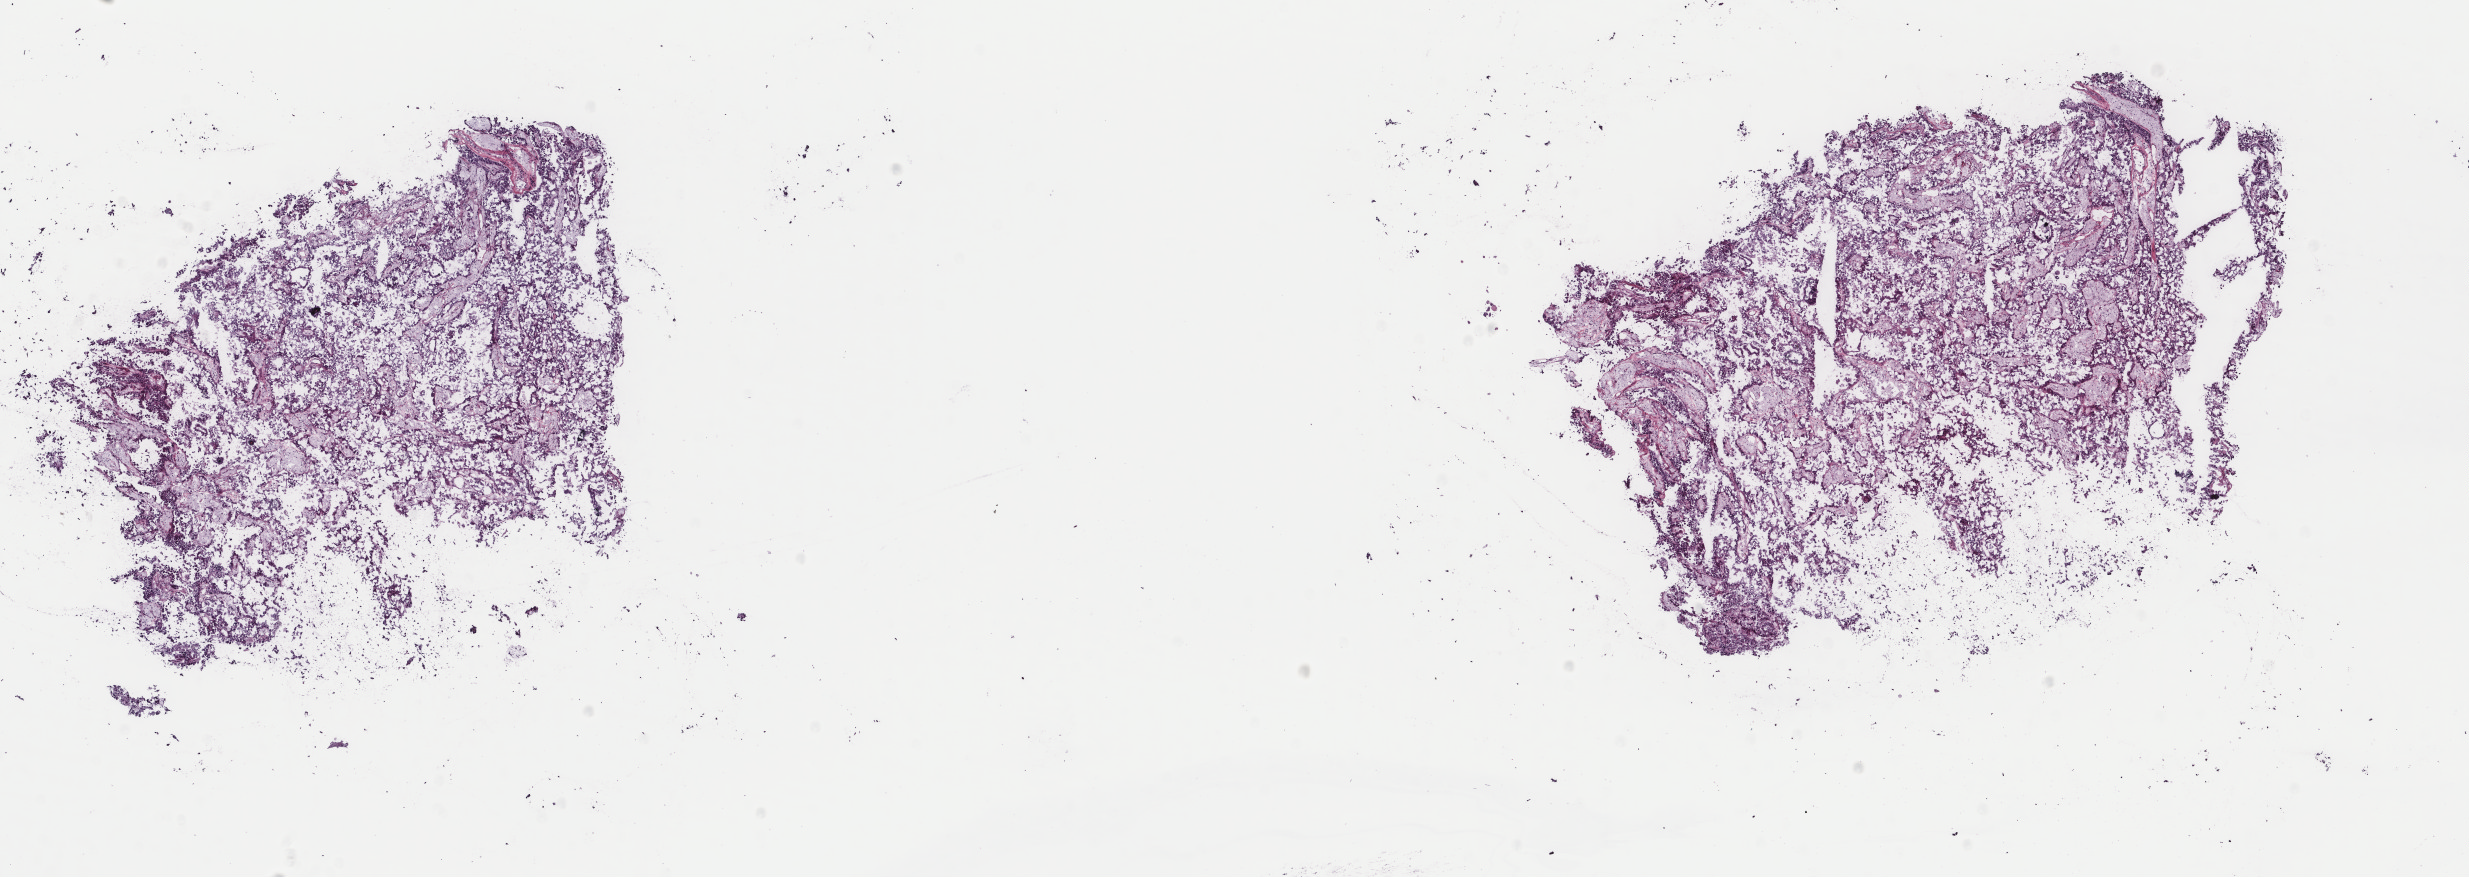
Digitized H&E-stained tissue section (whole slide) — low-resolution overview of the scanned area, about 19.6 x 7.0 mm (acquisition: 40x scan), frozen section from the top of the tissue portion, kidney, primary tumour sample. Patient sex: male. Composition of this section per pathologist review: tumour cells 100%, tumour nuclei 75%, normal cells 0%, stromal cells 0%, necrosis 0%. Infiltration values recorded for this section: lymphocyte infiltration 2%, monocyte infiltration 2%, neutrophil infiltration 0%.
Diagnosis: Papillary adenocarcinoma, NOS. AJCC pathologic stage: I (7th edition).